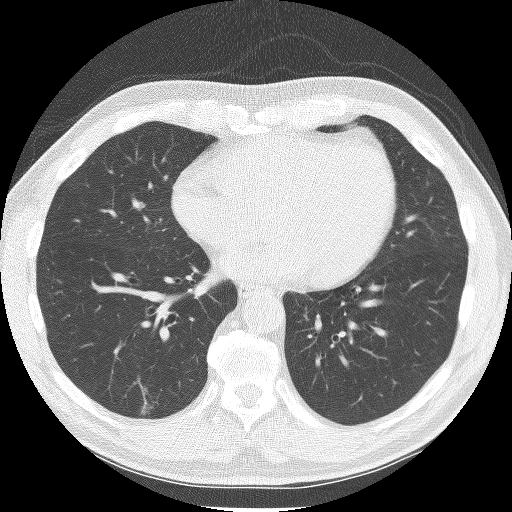
Axial slice from a low-dose chest CT screening exam. First (baseline) screen. Lung window (W 1500 / L -600 HU). 2.5 mm slice thickness. Lung (sharp) reconstruction kernel (BONE). Slice 90 of 150 in the series. 512 × 512 image matrix. Male, age 61 years at enrolment. Current smoker at enrolment.
Expert reader's lesion annotation, bounding box (x1, y1, x2, y2) in pixels: (124, 382, 166, 424). Screening reader's record for this exam (one nodule recorded; not confirmed to be the boxed lesion): non-calcified nodule or mass ≥4 mm, right lower lobe, 12 × 11 mm, spiculated (stellate) margins, soft tissue attenuation. Official screen result: positive, change unspecified: nodule(s) >= 4 mm or enlarging nodule(s), mass(es), or other non-specific abnormalities suspicious for lung cancer. Participant outcome: lung cancer diagnosed 232 days after this screen — adenocarcinoma, NOS, right lower lobe, moderately differentiated (G2), stage IA (AJCC 6th edition), 9 mm at pathology.